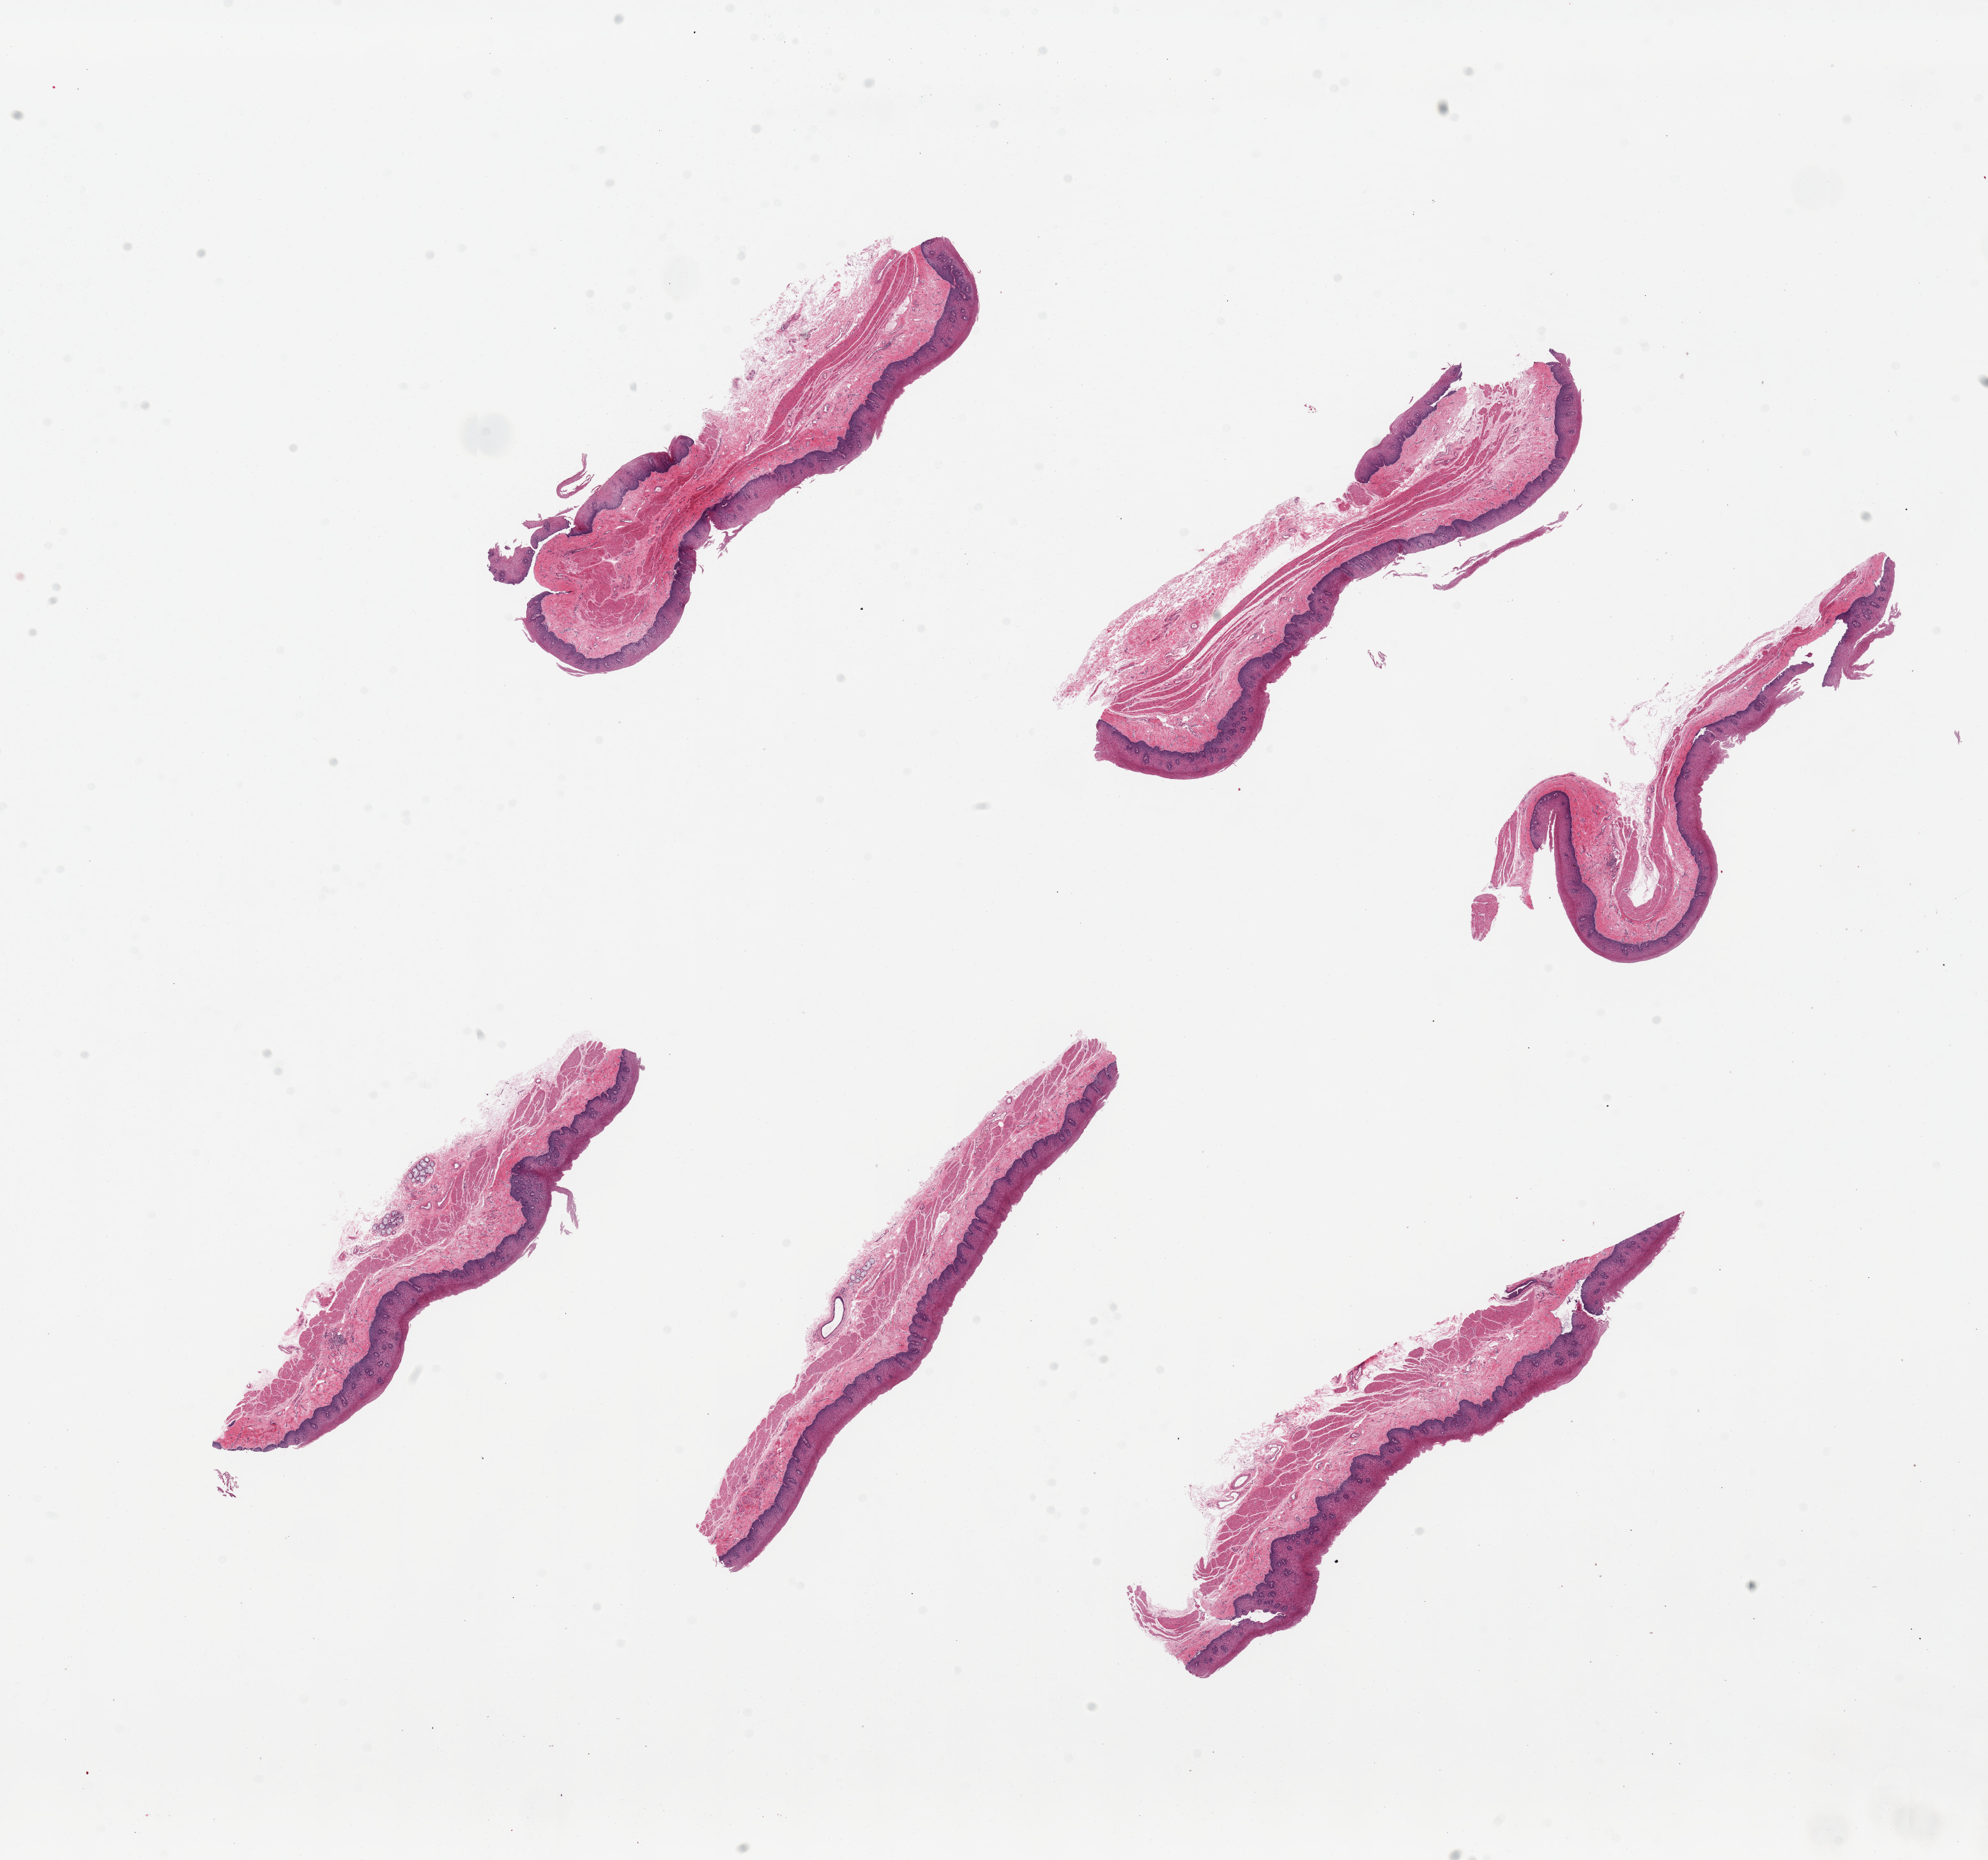
Whole-slide image, H&E stain, low-resolution overview of the scanned area, about 24.6 x 23.0 mm (acquisition: 20x scan), PAXgene-fixed paraffin-embedded (PFPE) section, sampled site (target tissue): esophageal mucous membrane, donor tissue sample. Female donor.
Pathologist's review note for this sample: 6 pieces, up to 8x2mm. Well dissected; some mechanical disruption.